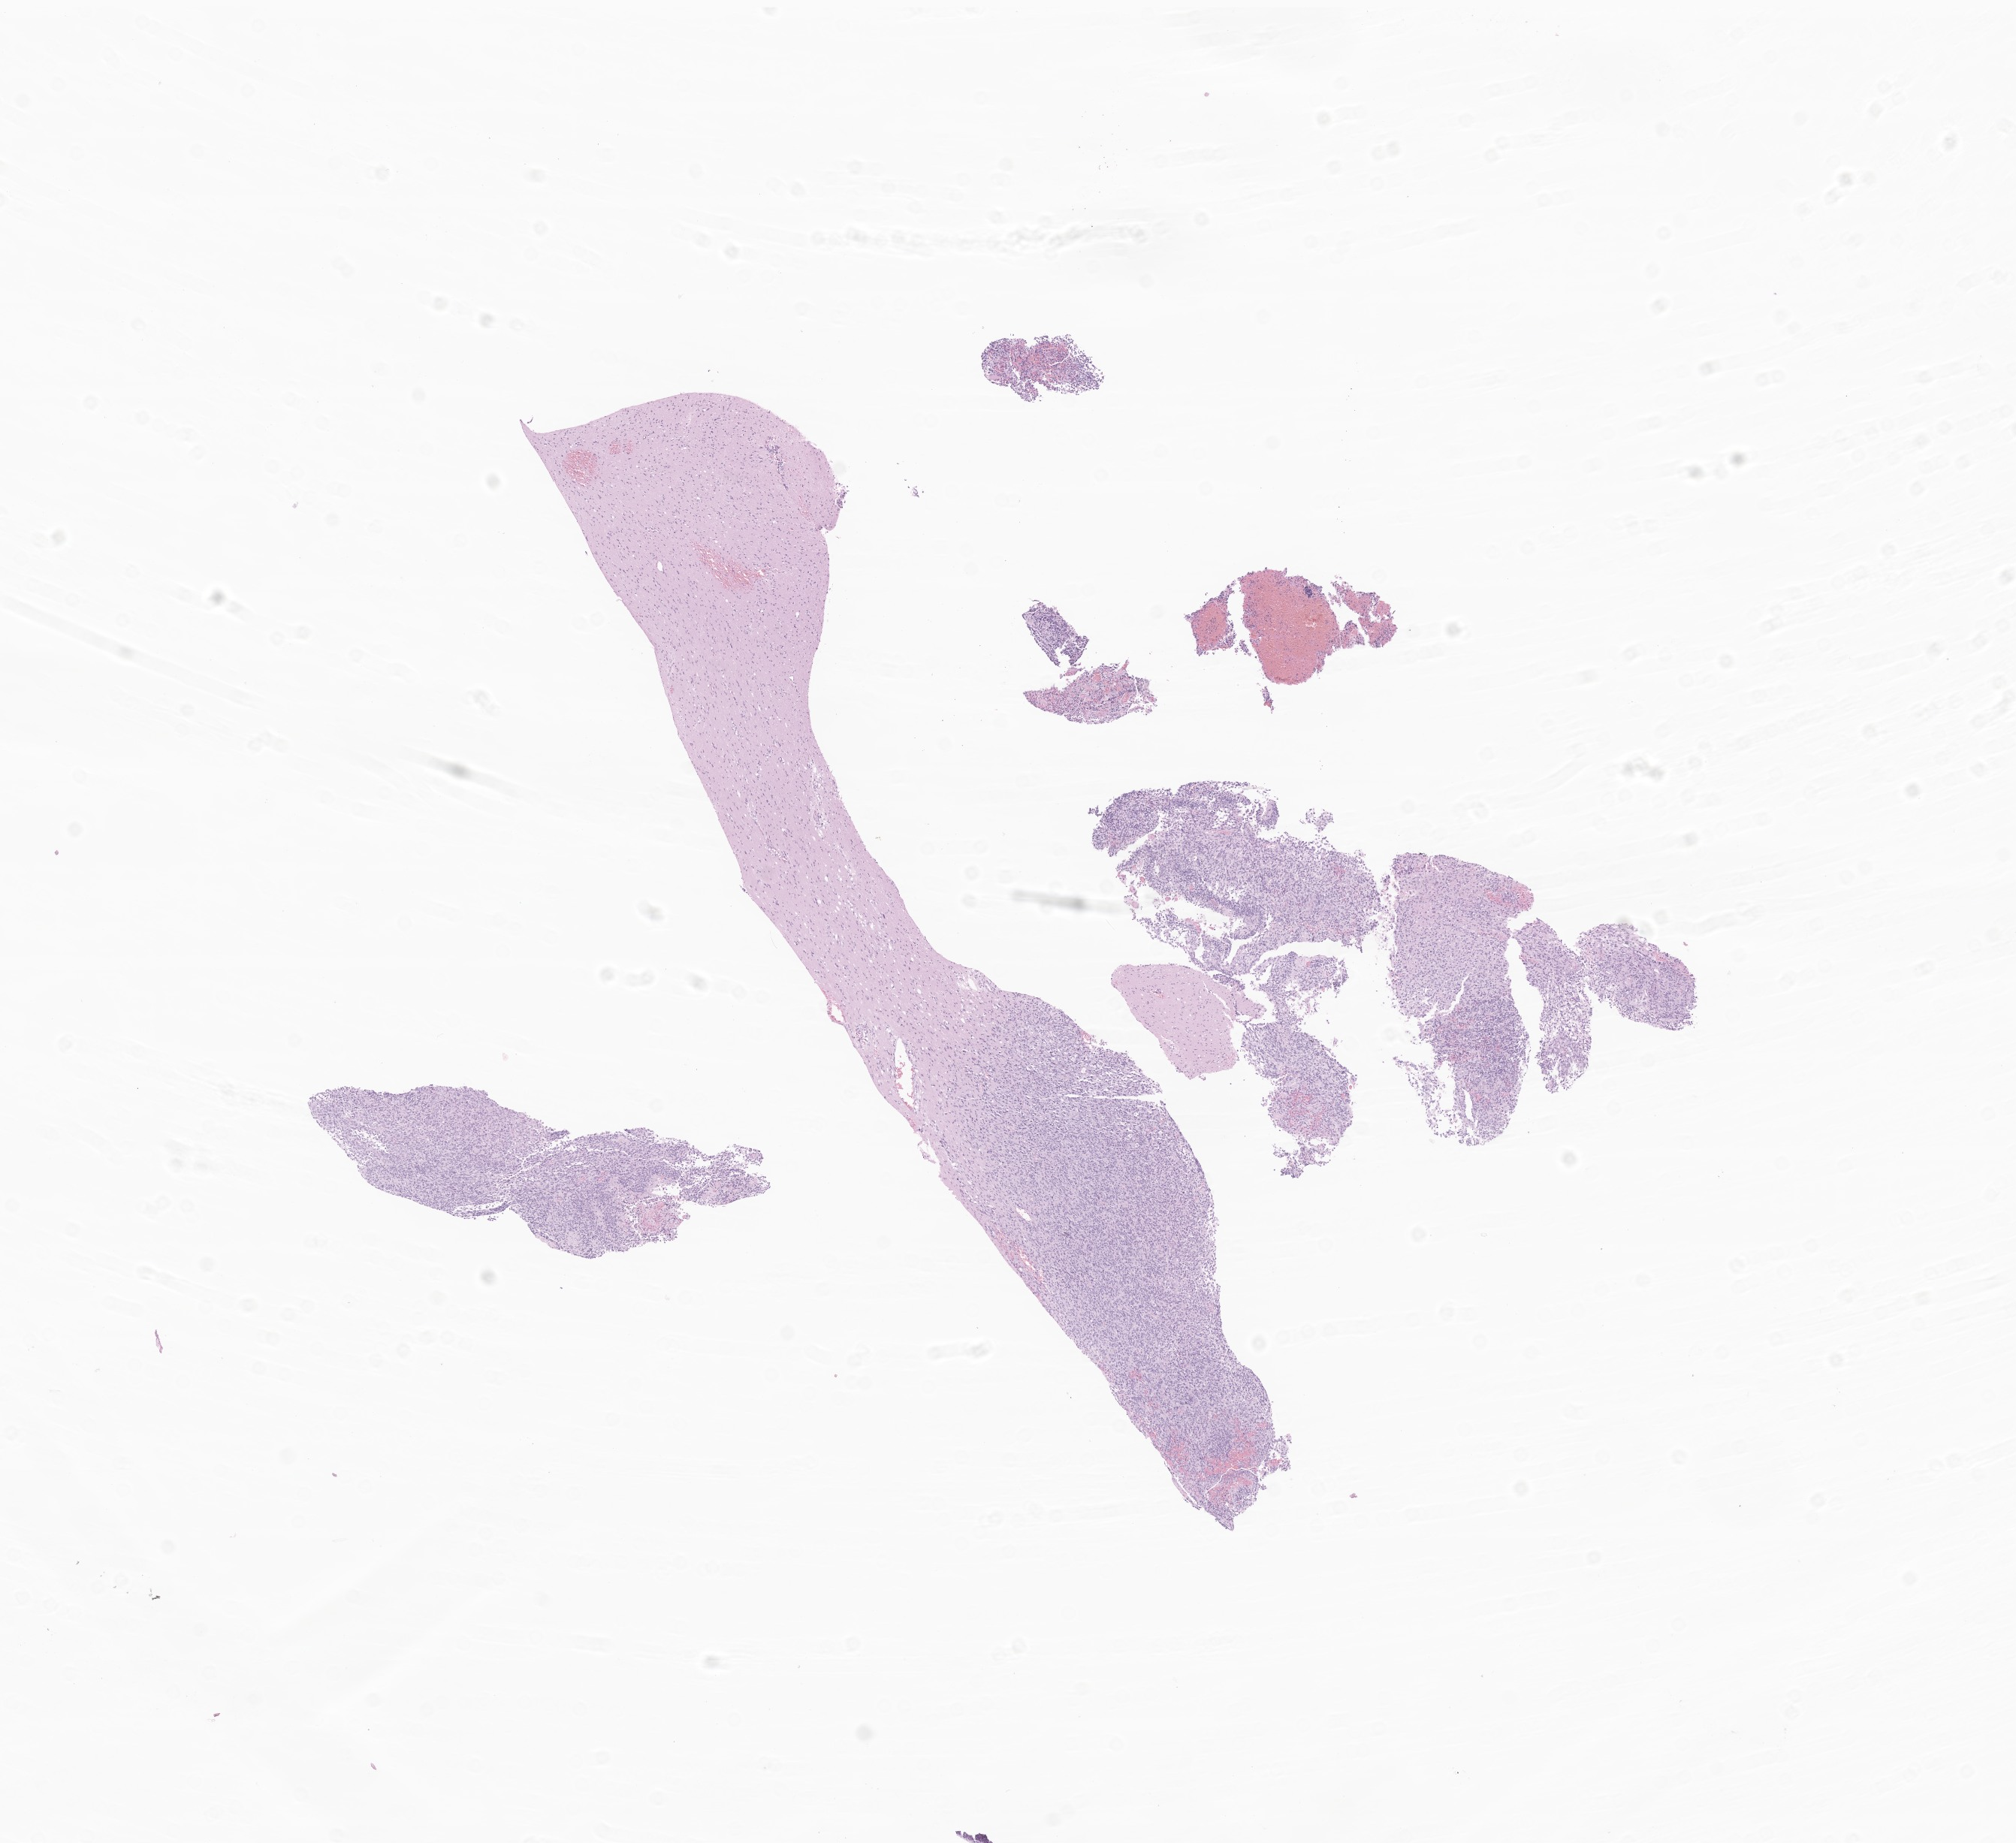
Digitized hematoxylin and eosin (H&E)-stained section of tumor tissue from the brain, shown as a low-resolution overview of the whole scanned area (about 11.3 x 10.3 mm). FFPE section. Patient male; age 187 months (15 years 7 months).
Diagnosis (ICD-O-3 morphology term): Glioma, malignant.